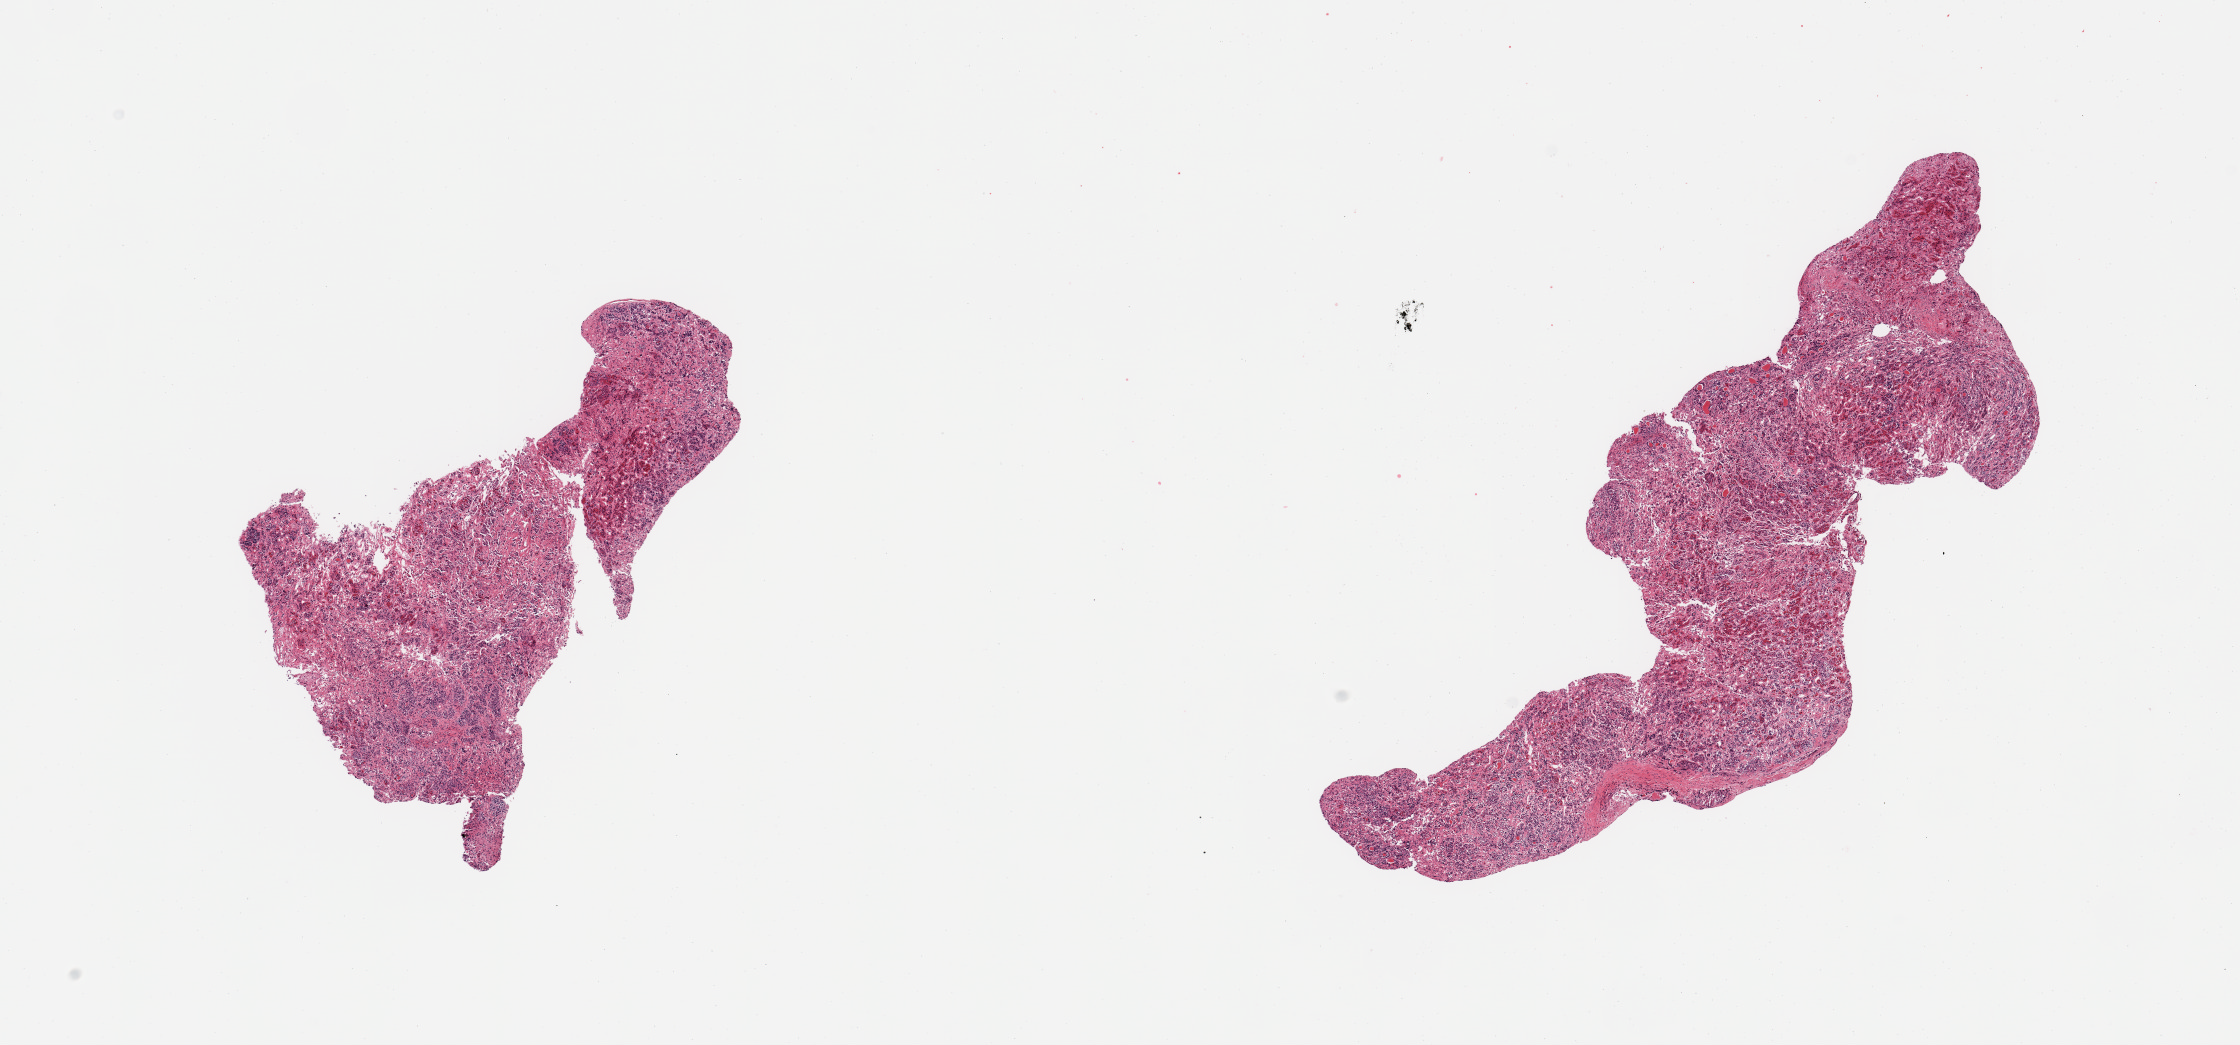
Whole-slide image, haematoxylin and eosin stain, brightfield — low-resolution overview of the scanned area, about 17.7 x 8.3 mm (acquisition: 20x scan), PAXgene-fixed paraffin-embedded (PFPE) section, sampled site (target tissue): pituitary, tissue donor sample. Donor: female.
Reviewer comment on this tissue sample: 2 pieces; all adenohypophysis, no neural tissue.